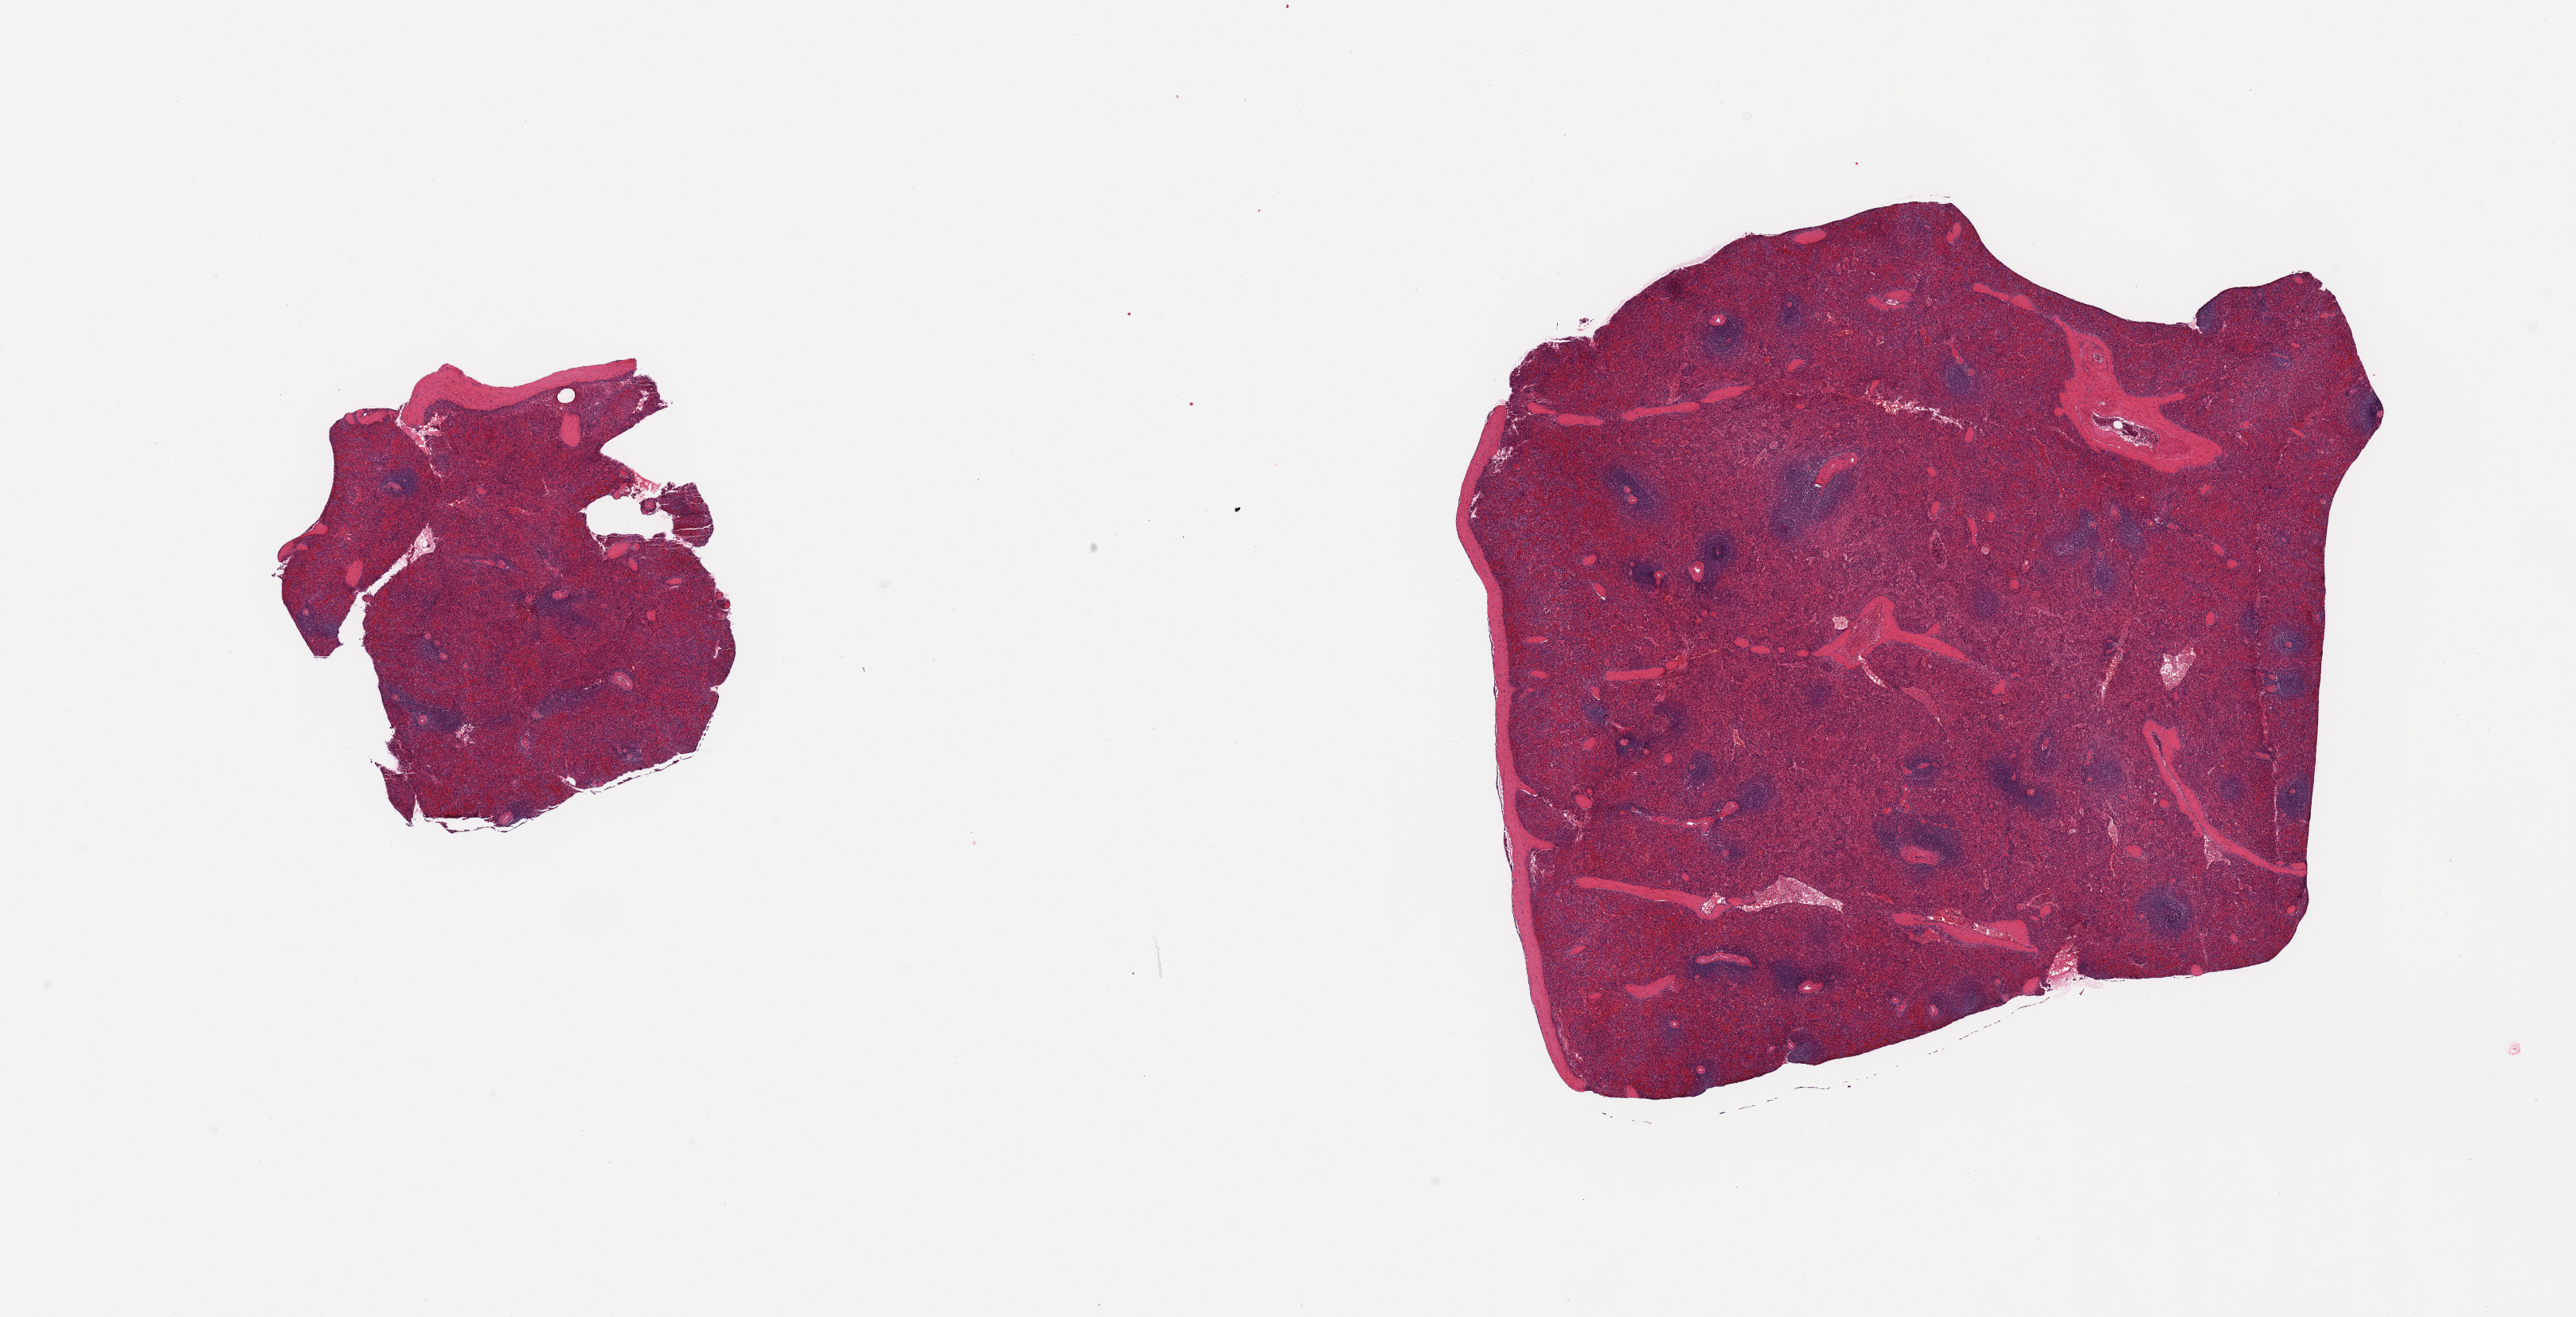
Whole-slide image, H&E stain, brightfield — low-resolution overview of the scanned area, about 25.6 x 13.1 mm (acquisition: 20x scan), PAXgene-fixed, paraffin-embedded tissue, sampled site (target tissue): spleen, donor tissue sample. Male donor.
Reviewer comment on this tissue sample: 2 pieces; congestion; capsule included.